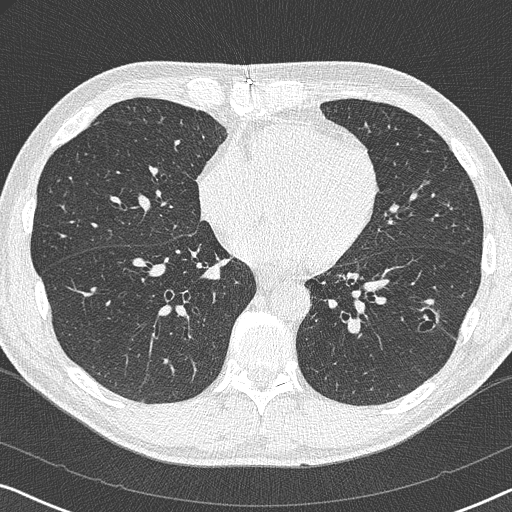
Low-dose screening chest CT, axial slice. Baseline annual screen. Lung window (W 1500 / L -600 HU). 1 mm slice thickness. Lung (sharp) reconstruction kernel (B50f). 120 kVp. Slice 206 of 327 in the series. 512 × 512 image matrix, field of view 330 × 330 mm. Male, age 59 years at enrolment. Current smoker at enrolment.
Expert reader's lesion annotation, bounding box [x1, y1, x2, y2] px = [413, 302, 451, 339]. The screening reader recorded 2 non-calcified nodules or masses ≥4 mm on this exam; which of them this box marks is not recorded. Participant outcome: lung cancer diagnosed 821 days after this screen (after the third annual screen) — adenocarcinoma, NOS, left lower lobe, poorly differentiated (G3), stage IA (AJCC 6th edition), 20 mm at pathology.